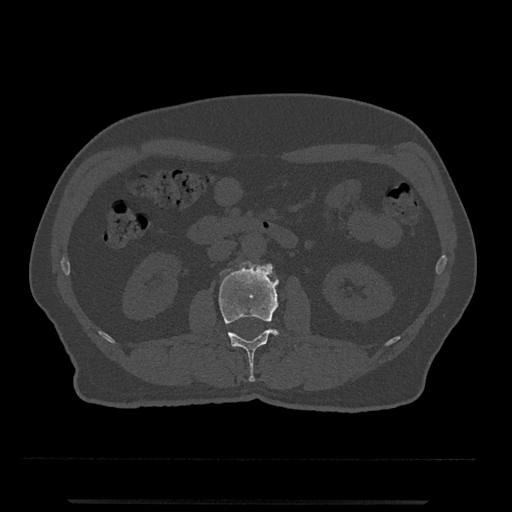
CT including the spine, one axial slice; bone window (W 1800 / L 400 HU); 0.5 mm slice thickness; 512 × 512 image matrix. Male patient, age 63 years. From the clinical record (not read from this slice): primary cancer: prostate.
Annotated regions visible in this slice (semi-automatic segmentation, software-assisted and operator-edited):
- L2 vertebra: bounding box (x1, y1, x2, y2) in pixels: (218, 261, 305, 382)